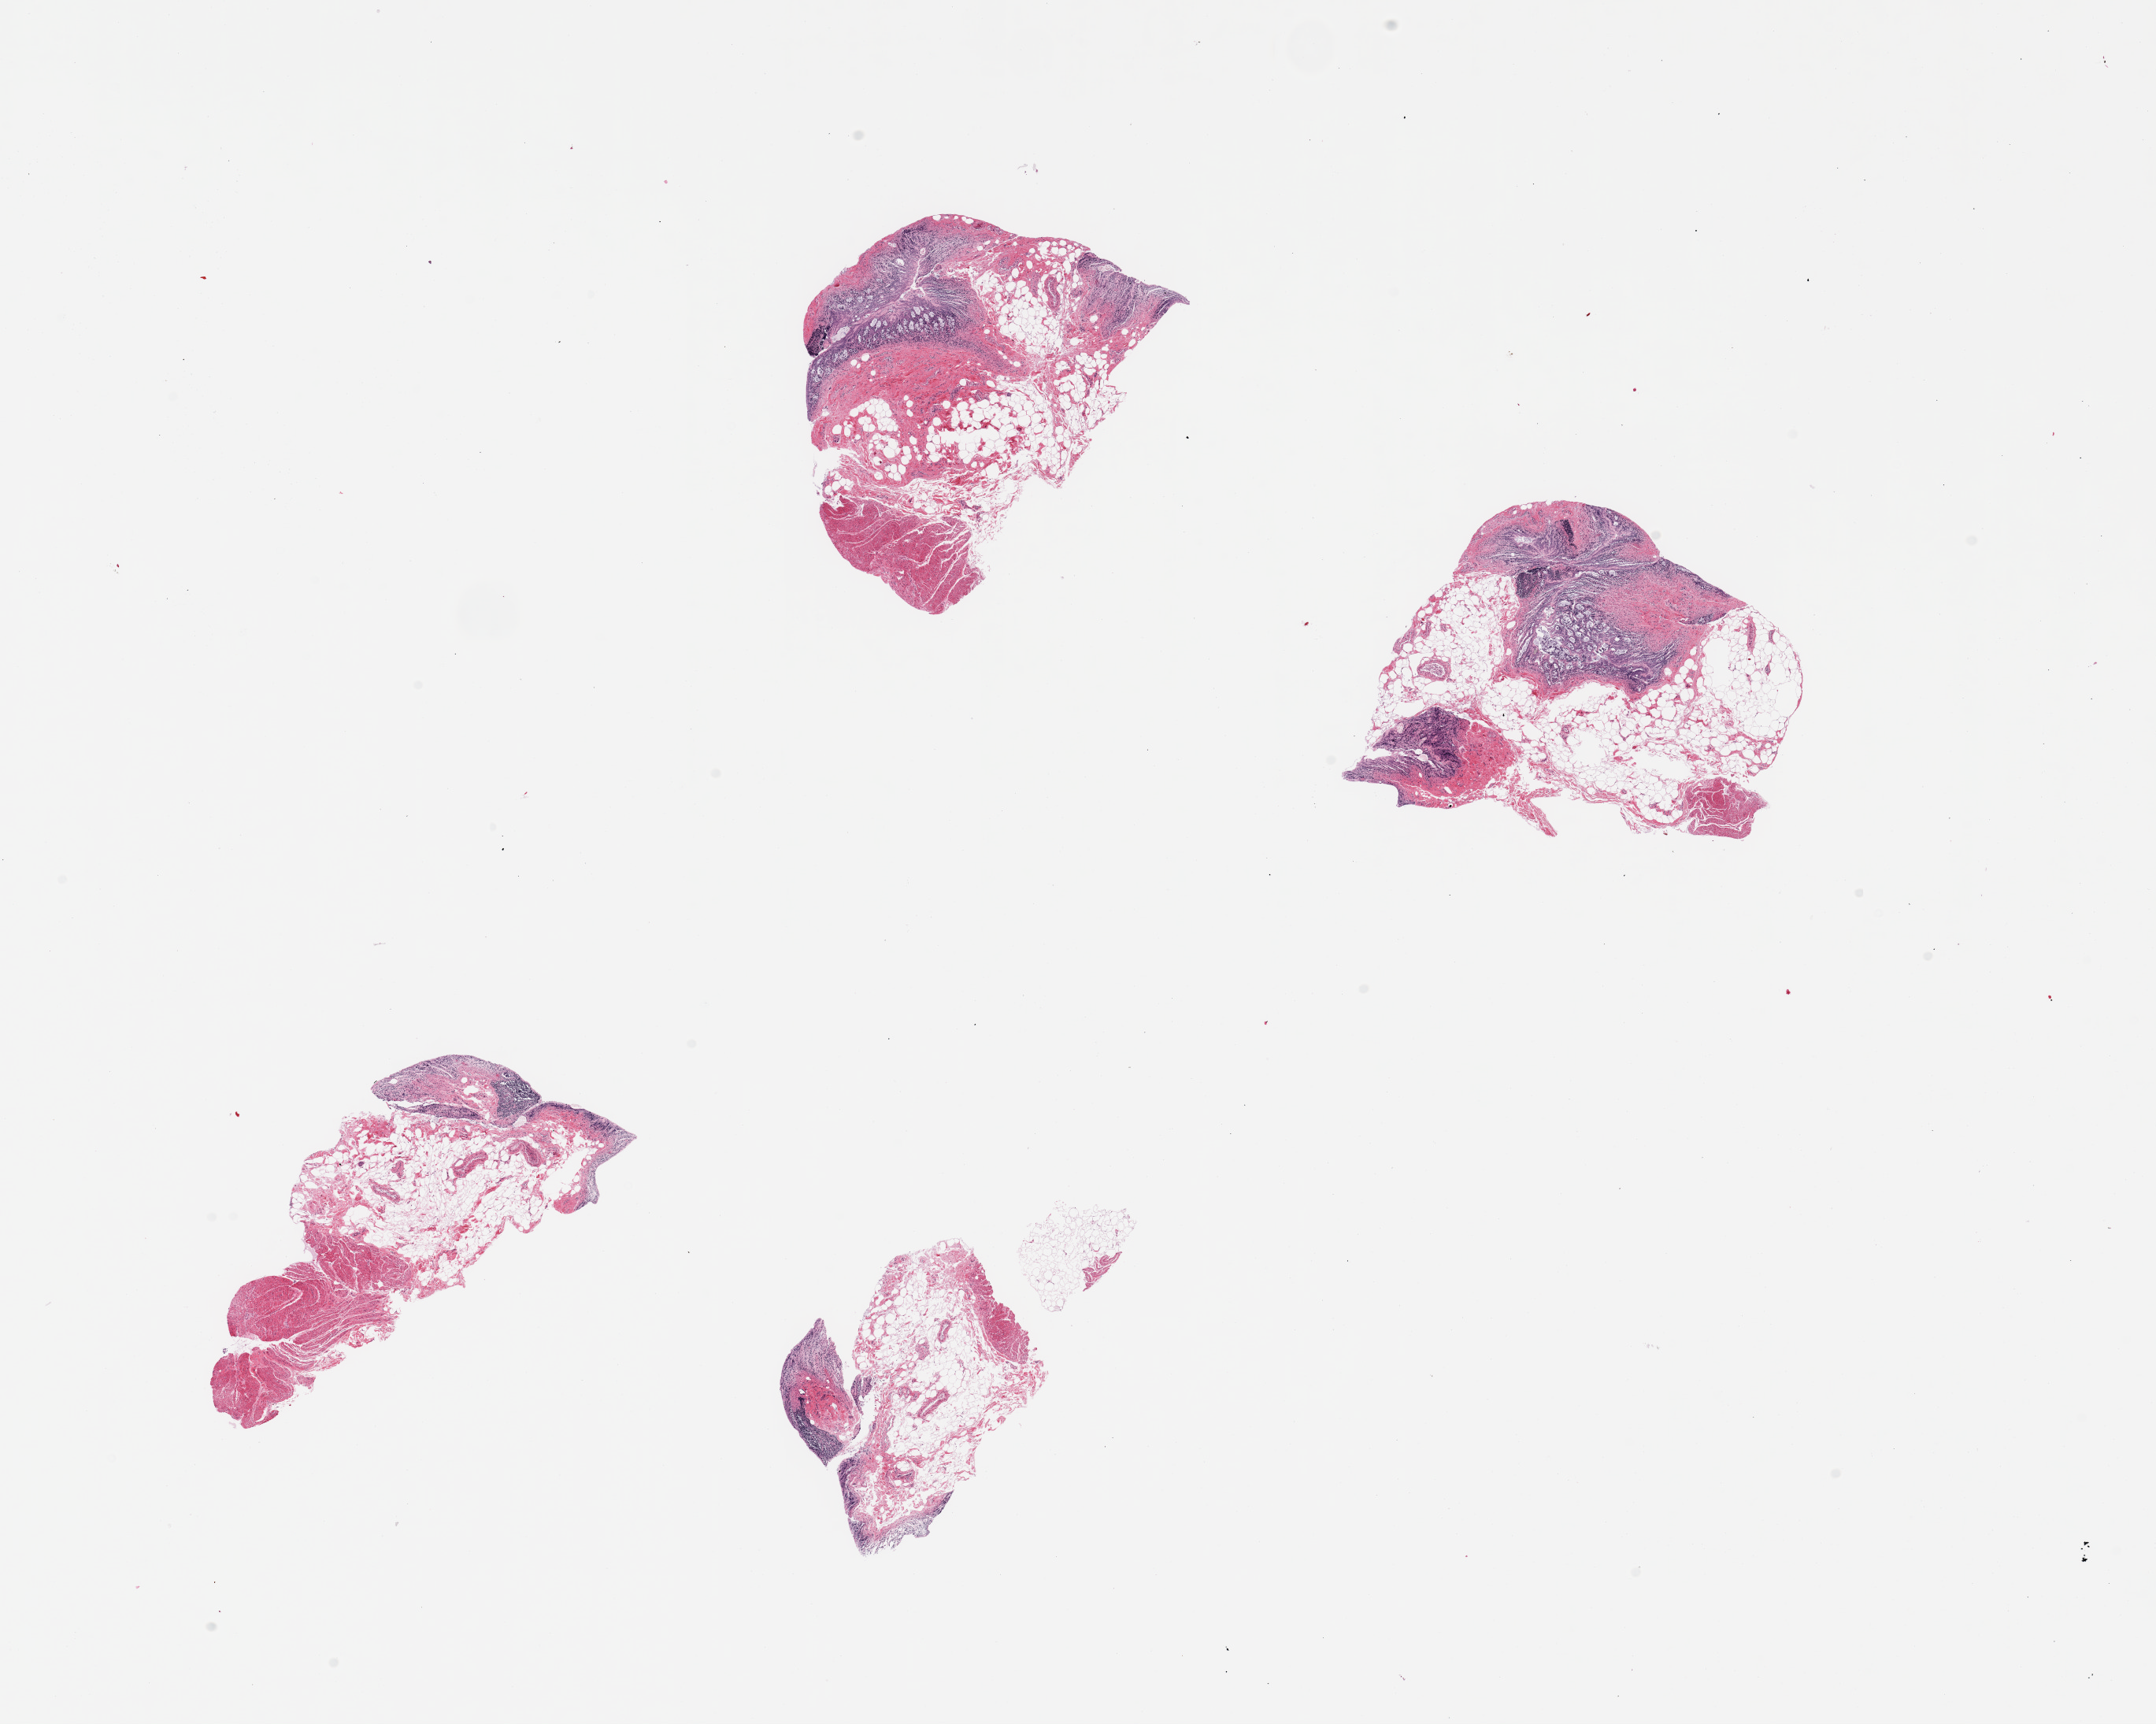
Digitized haematoxylin and eosin-stained section, shown as a low-resolution overview of the whole scanned area (about 21.7 x 17.3 mm); PAXgene-fixed, paraffin-embedded tissue; sampled site (target tissue): sigmoid colon; donor tissue sample.
• pathologist's review note for this sample: 4 pieces; all contain autolyzed mucosa; minimal muscularis